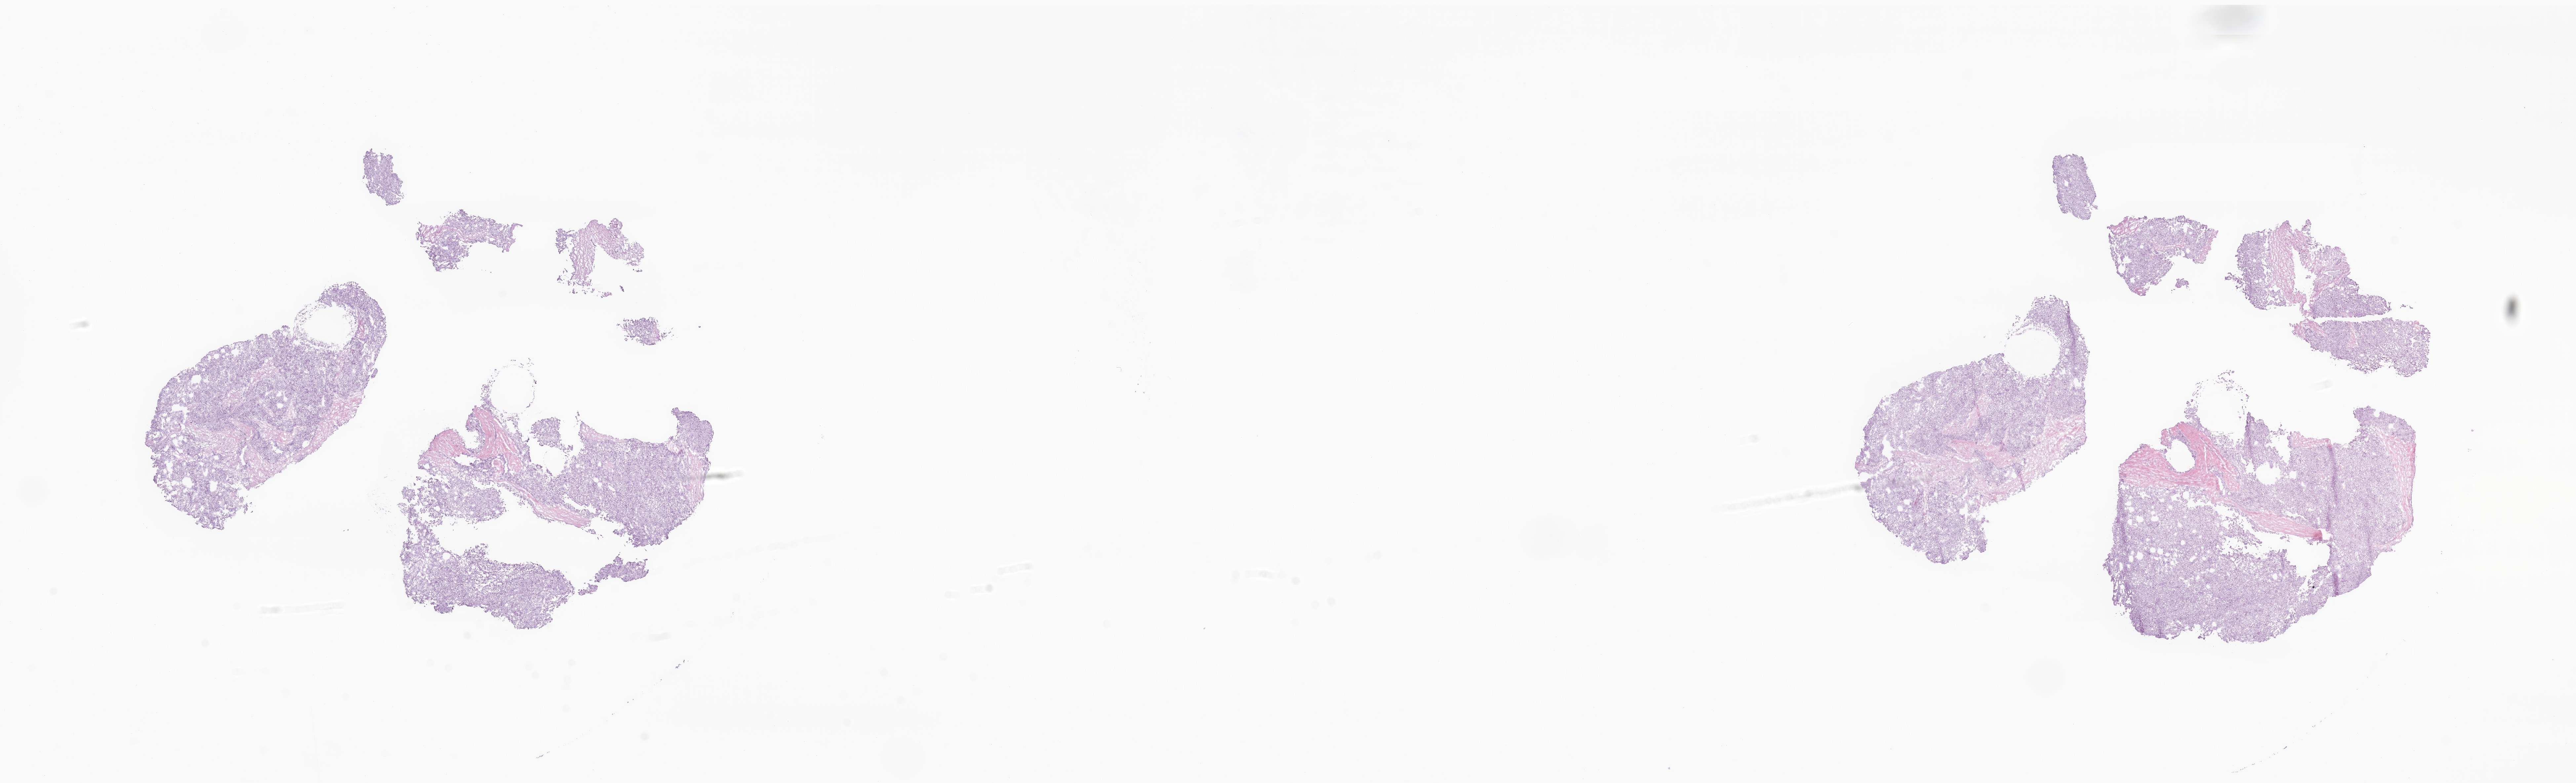
Digitized haematoxylin and eosin-stained section of tumor tissue from the soft tissue of lower extremity — a low-resolution overview of the entire scanned area, about 32.9 x 10.0 mm. Cryosection (OCT / tissue freezing medium). Patient male; age 161 months (13 years 5 months).
Diagnosis: Alveolar soft part sarcoma.